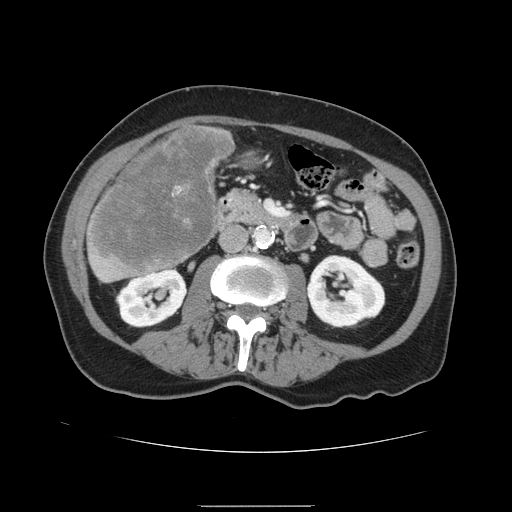
Contrast-enhanced abdominal CT, one axial slice; slice 43 of 168 in the series (ordered by position); 120 kVp; intravenous contrast given; soft-tissue window (W 400 / L 40 HU); 2.5 mm slice thickness; 512 × 512 image matrix, field of view 386 × 386 mm. Male patient, age 74 years. Case-level facts recorded for this patient, not image findings: diagnosis: colorectal cancer liver metastases, imaged before liver resection; multiple liver metastases: no; largest metastasis: 14.5 cm; disease in both lobes: yes.
Structures marked on this image (manually delineated by an expert):
- liver: bounding box <86,125,234,283> (left, top, right, bottom; pixels)
- liver metastasis: <90,130,231,271>